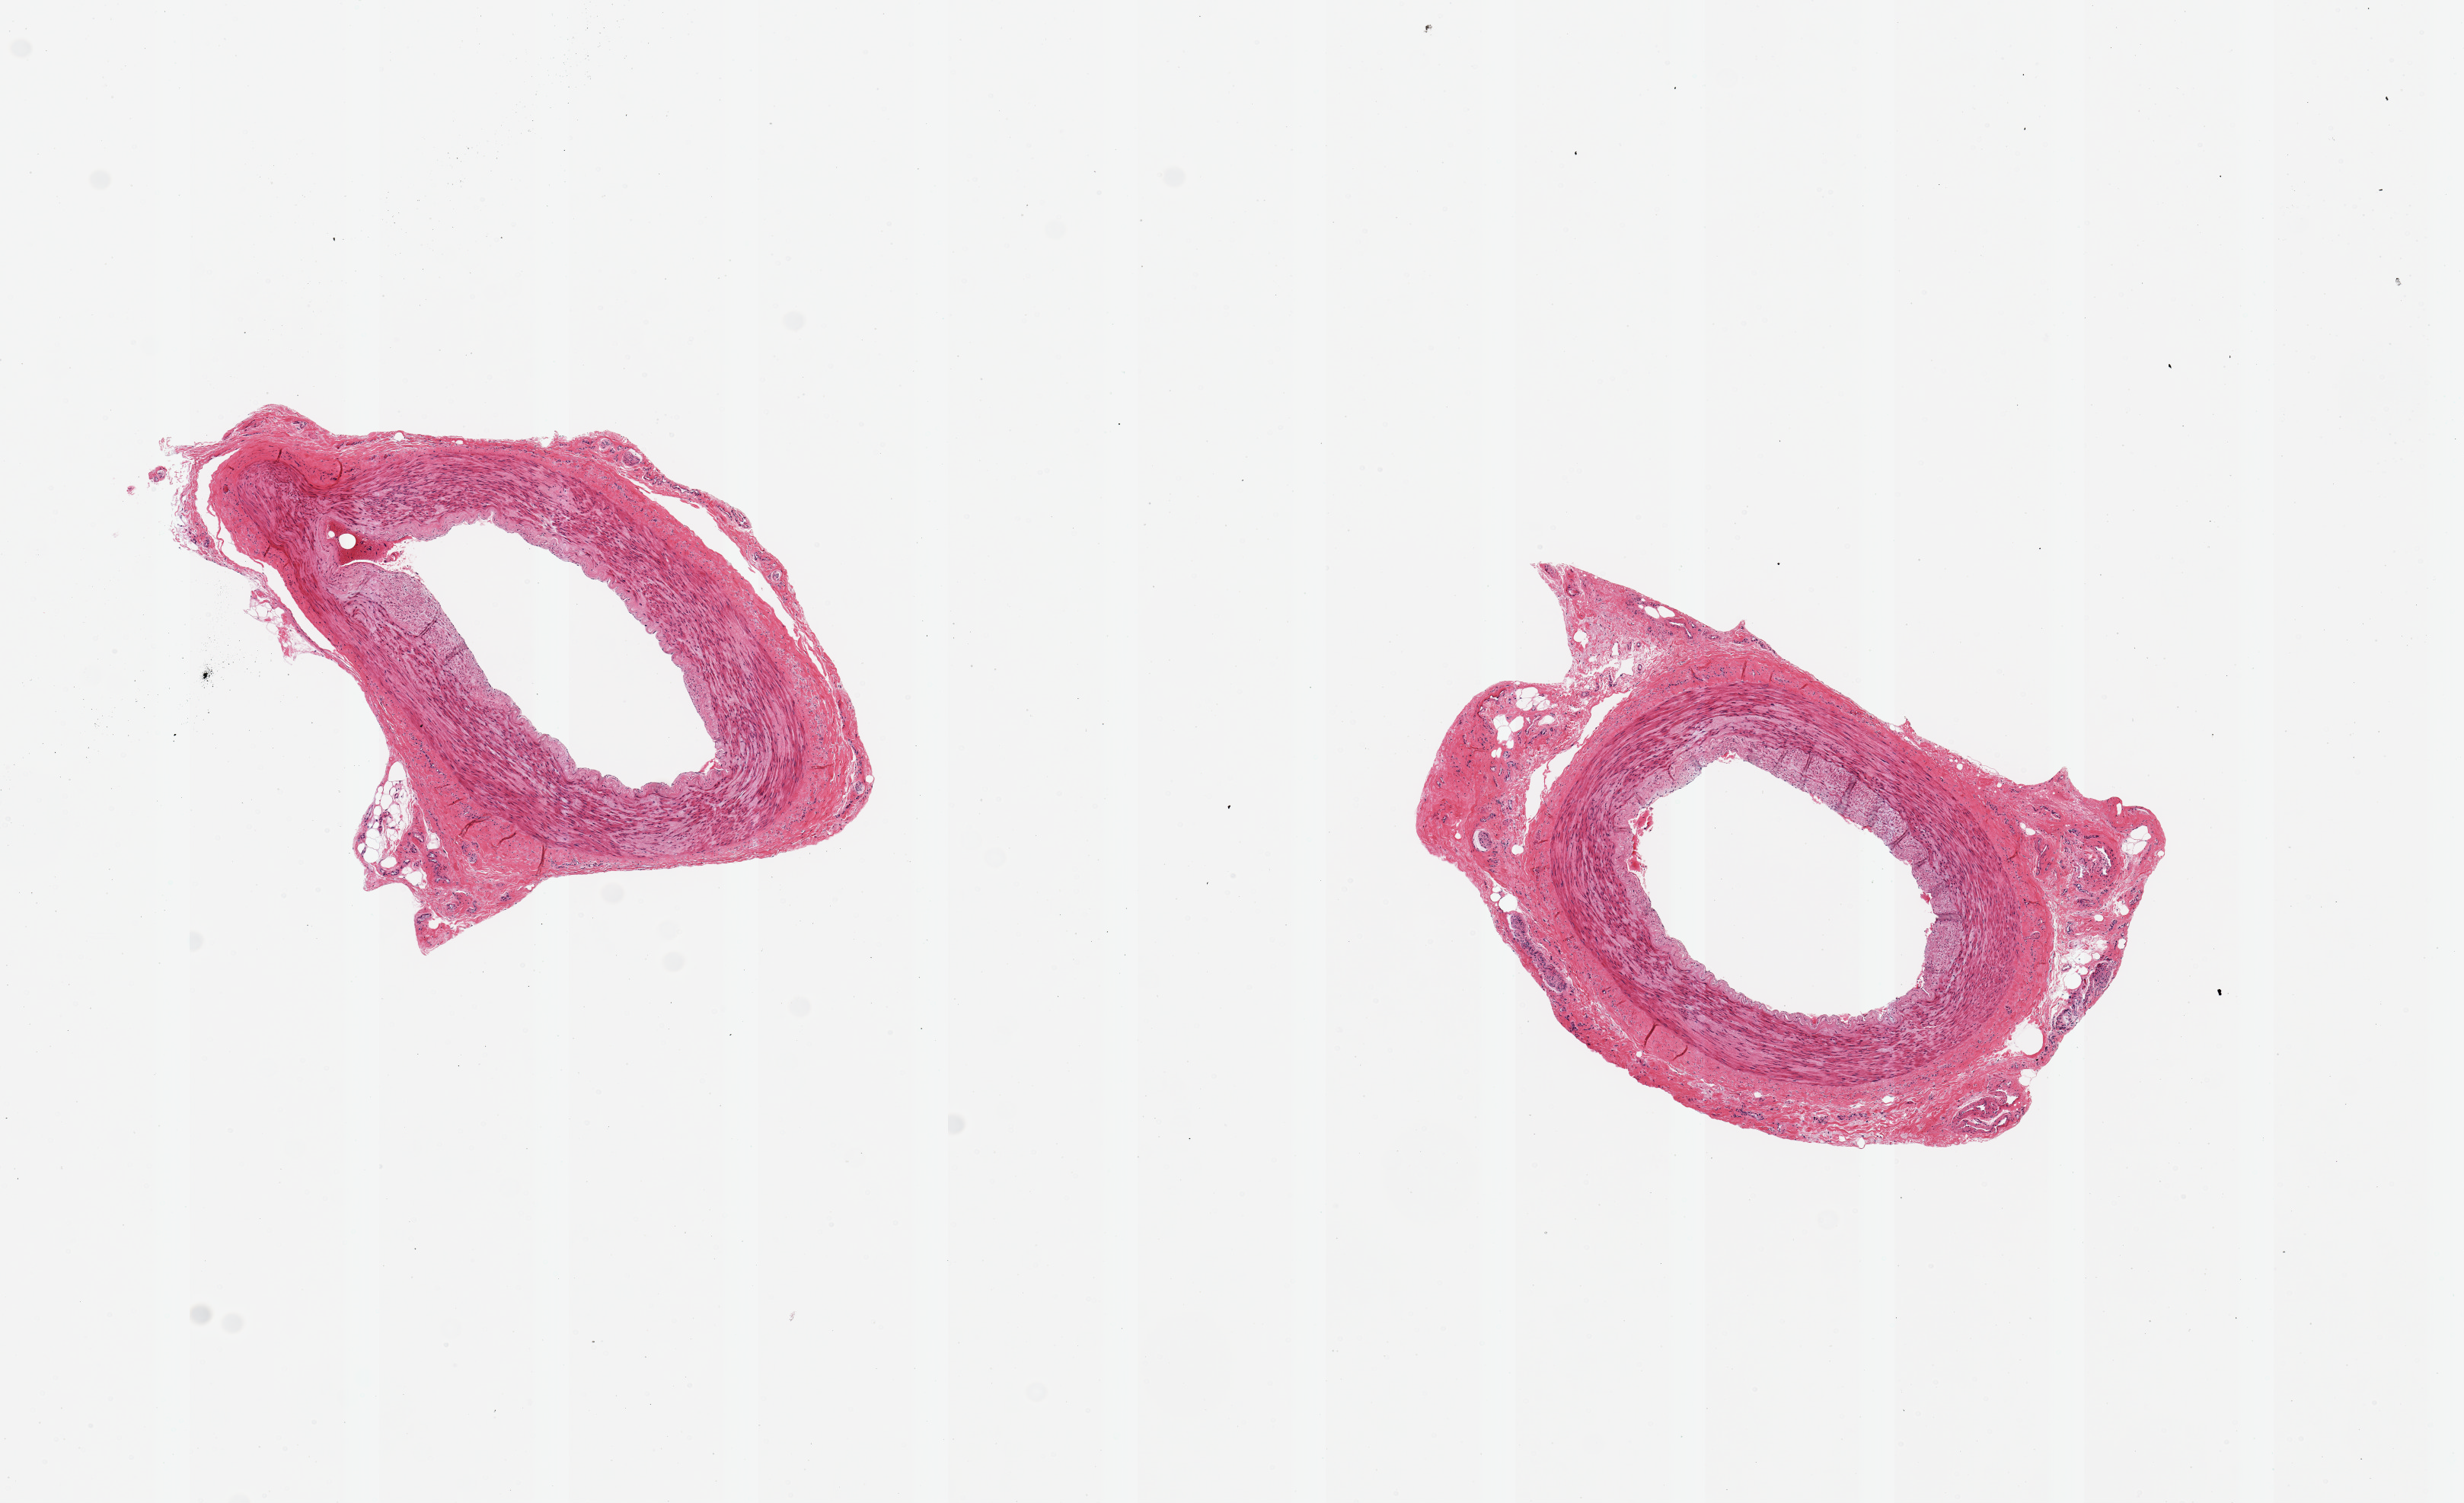
Whole-slide image, hematoxylin and eosin (H&E) stain, low-resolution overview of the scanned area, about 12.8 x 7.8 mm (acquisition: 20x scan). PAXgene-fixed, paraffin-embedded tissue. Section of tibial artery (target tissue). Donor tissue sample.
Review note (as recorded): 2 pieces ~2.5mm d. good clean specimens.